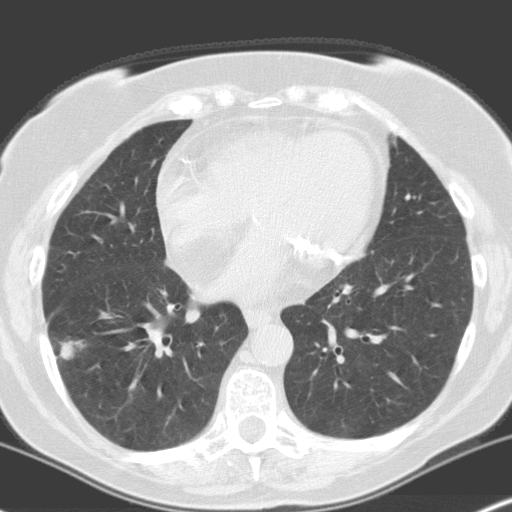
Low-dose screening chest CT, one axial slice. Slice 74 of 160 in the series (ordered by position). Lung window (W 1500 / L -600 HU). 512 × 512 image matrix.
Structures marked on this image (manually delineated by an expert):
- lesion 1 (tumor, lower lobe of right lung): bounding box <60,341,82,359> (left, top, right, bottom; pixels)